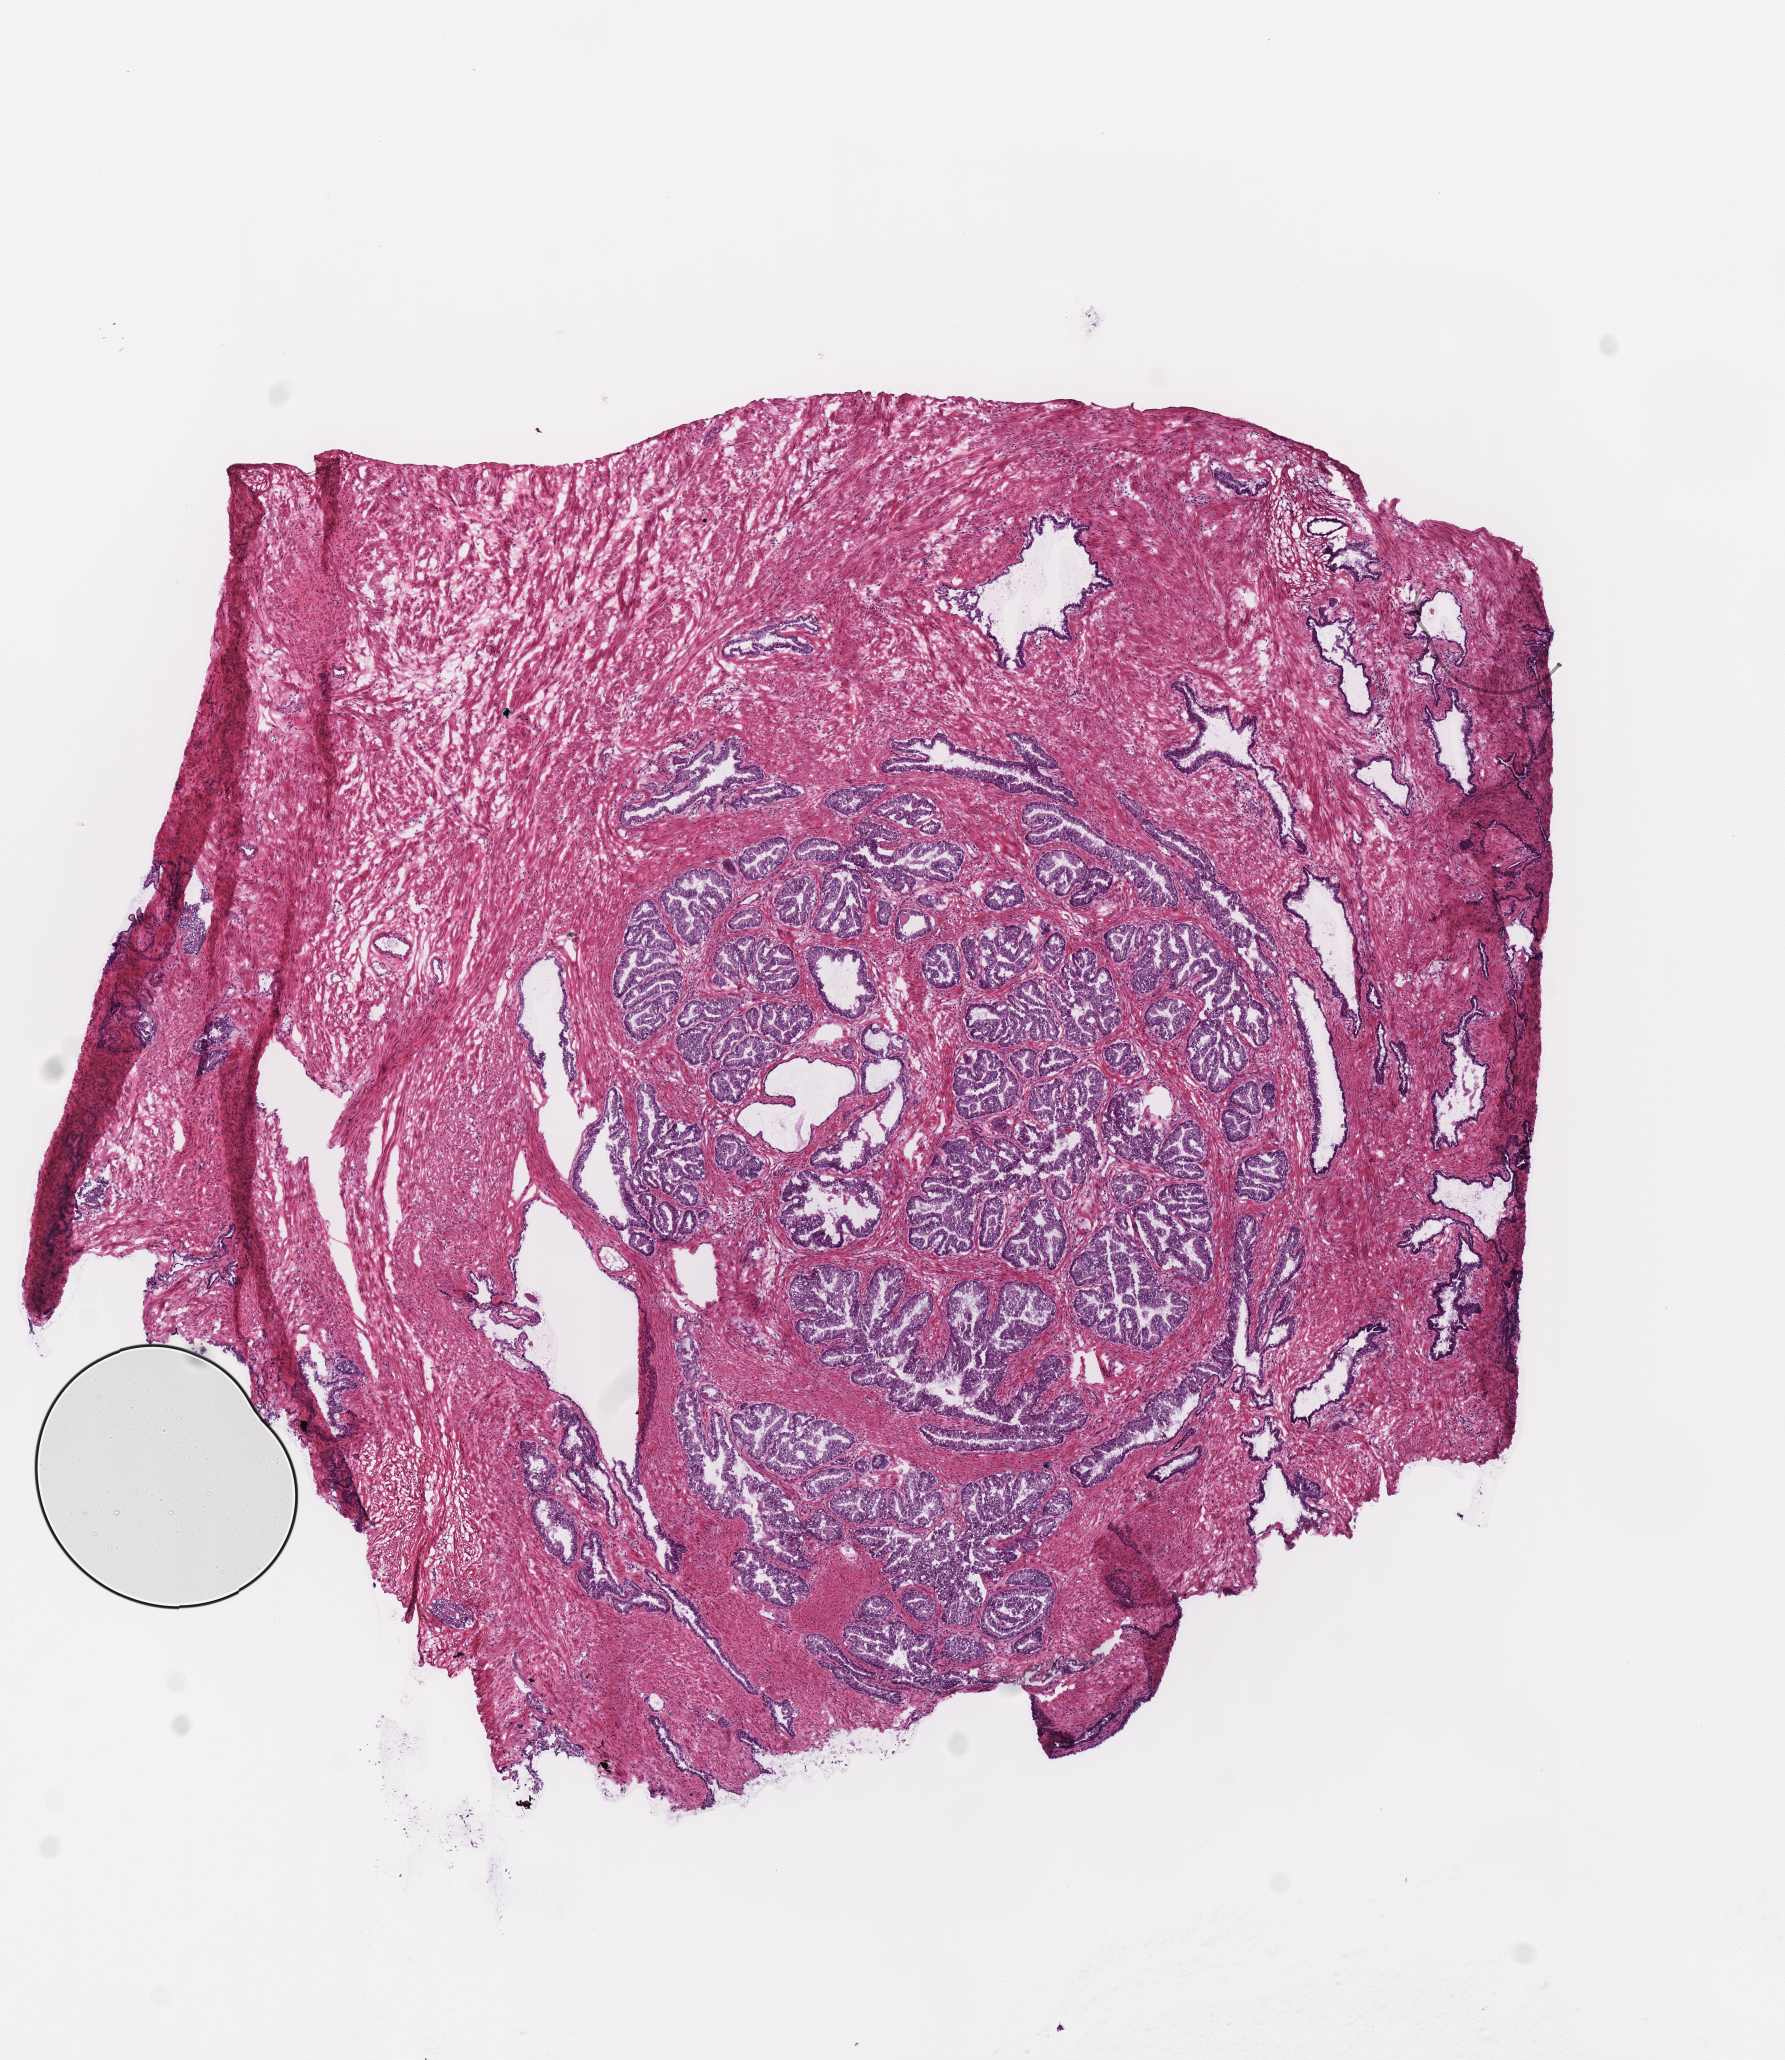
Hematoxylin and eosin (H&E) stained whole-slide image, a low-resolution overview of the entire scanned area, about 7.0 x 8.1 mm (slide scanned at 40x); frozen section from the top of the tissue portion; prostate, solid tissue normal (non-tumour tissue) sample. Male patient; age at initial diagnosis 53 years.
* this section: solid tissue normal (non-tumour) sample from the same patient
* patient diagnosis: Acinar cell carcinoma (prostate gland)